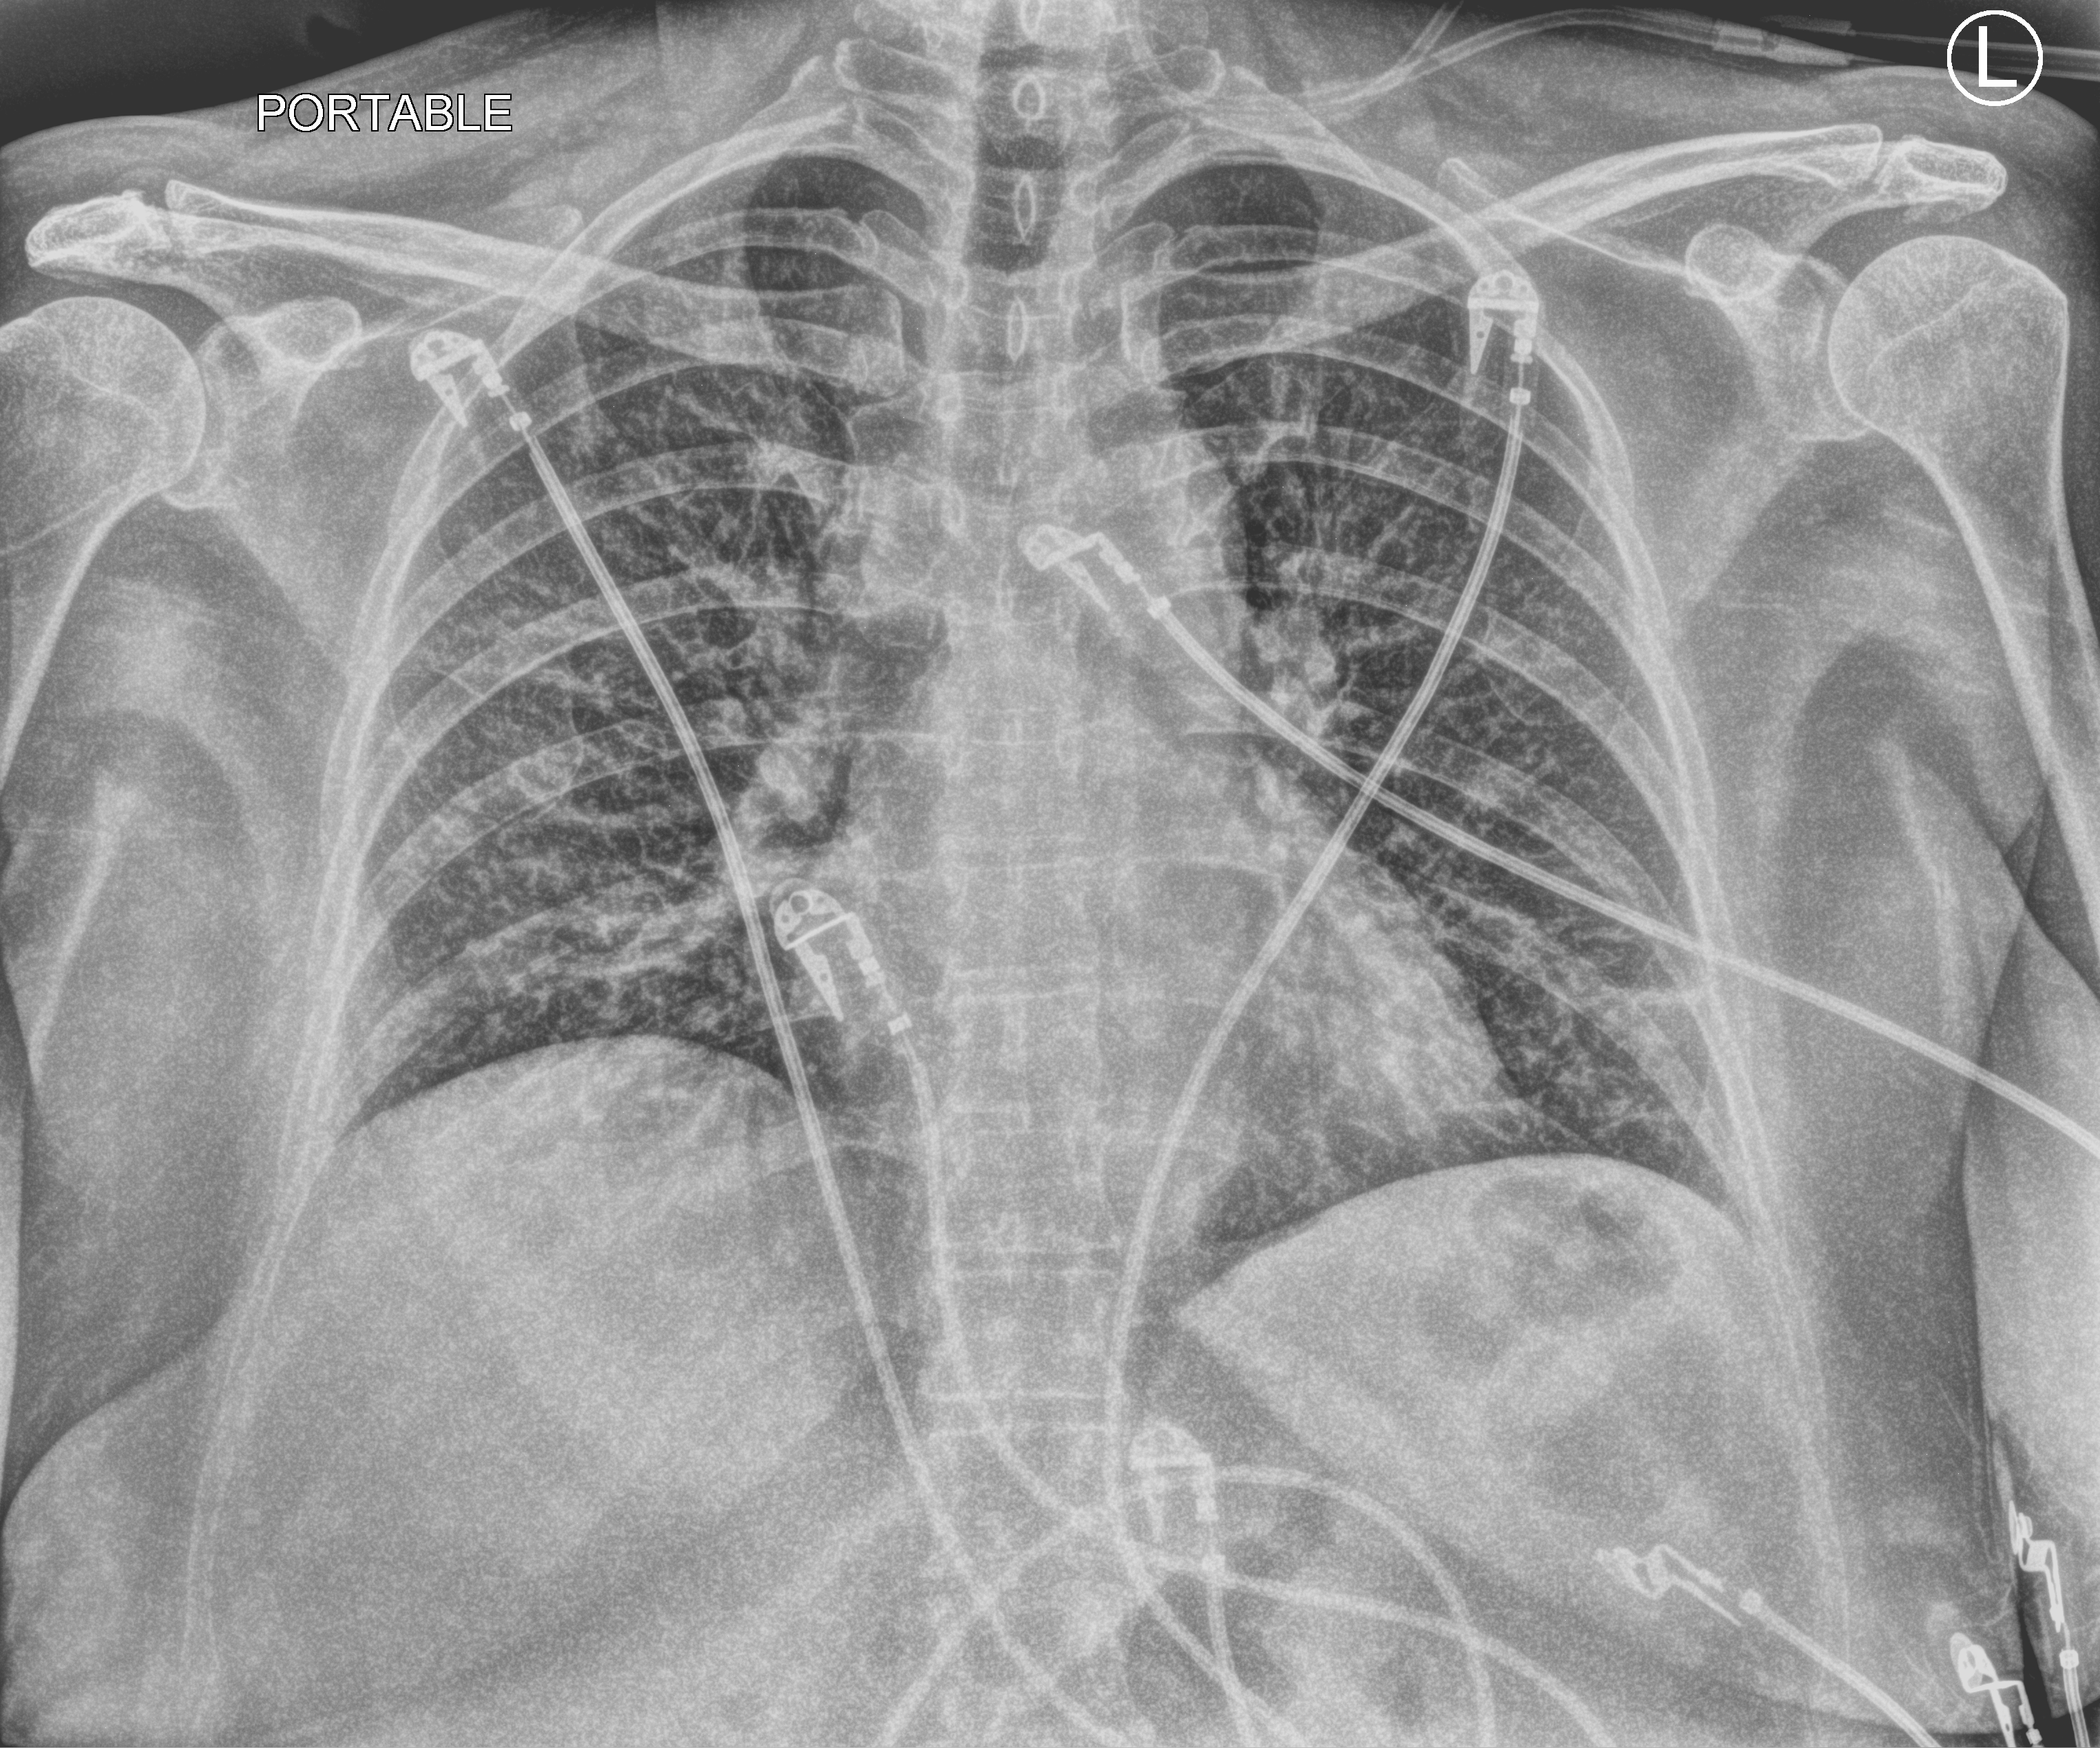
Portable chest radiograph. Patient hospitalised with COVID-19; female, aged 60–74 years.
From the hospital-stay record, not from the radiograph (when in the stay this image was taken is not recorded): mechanically ventilated during this hospital stay: yes; admitted to intensive care during this hospital stay: yes.